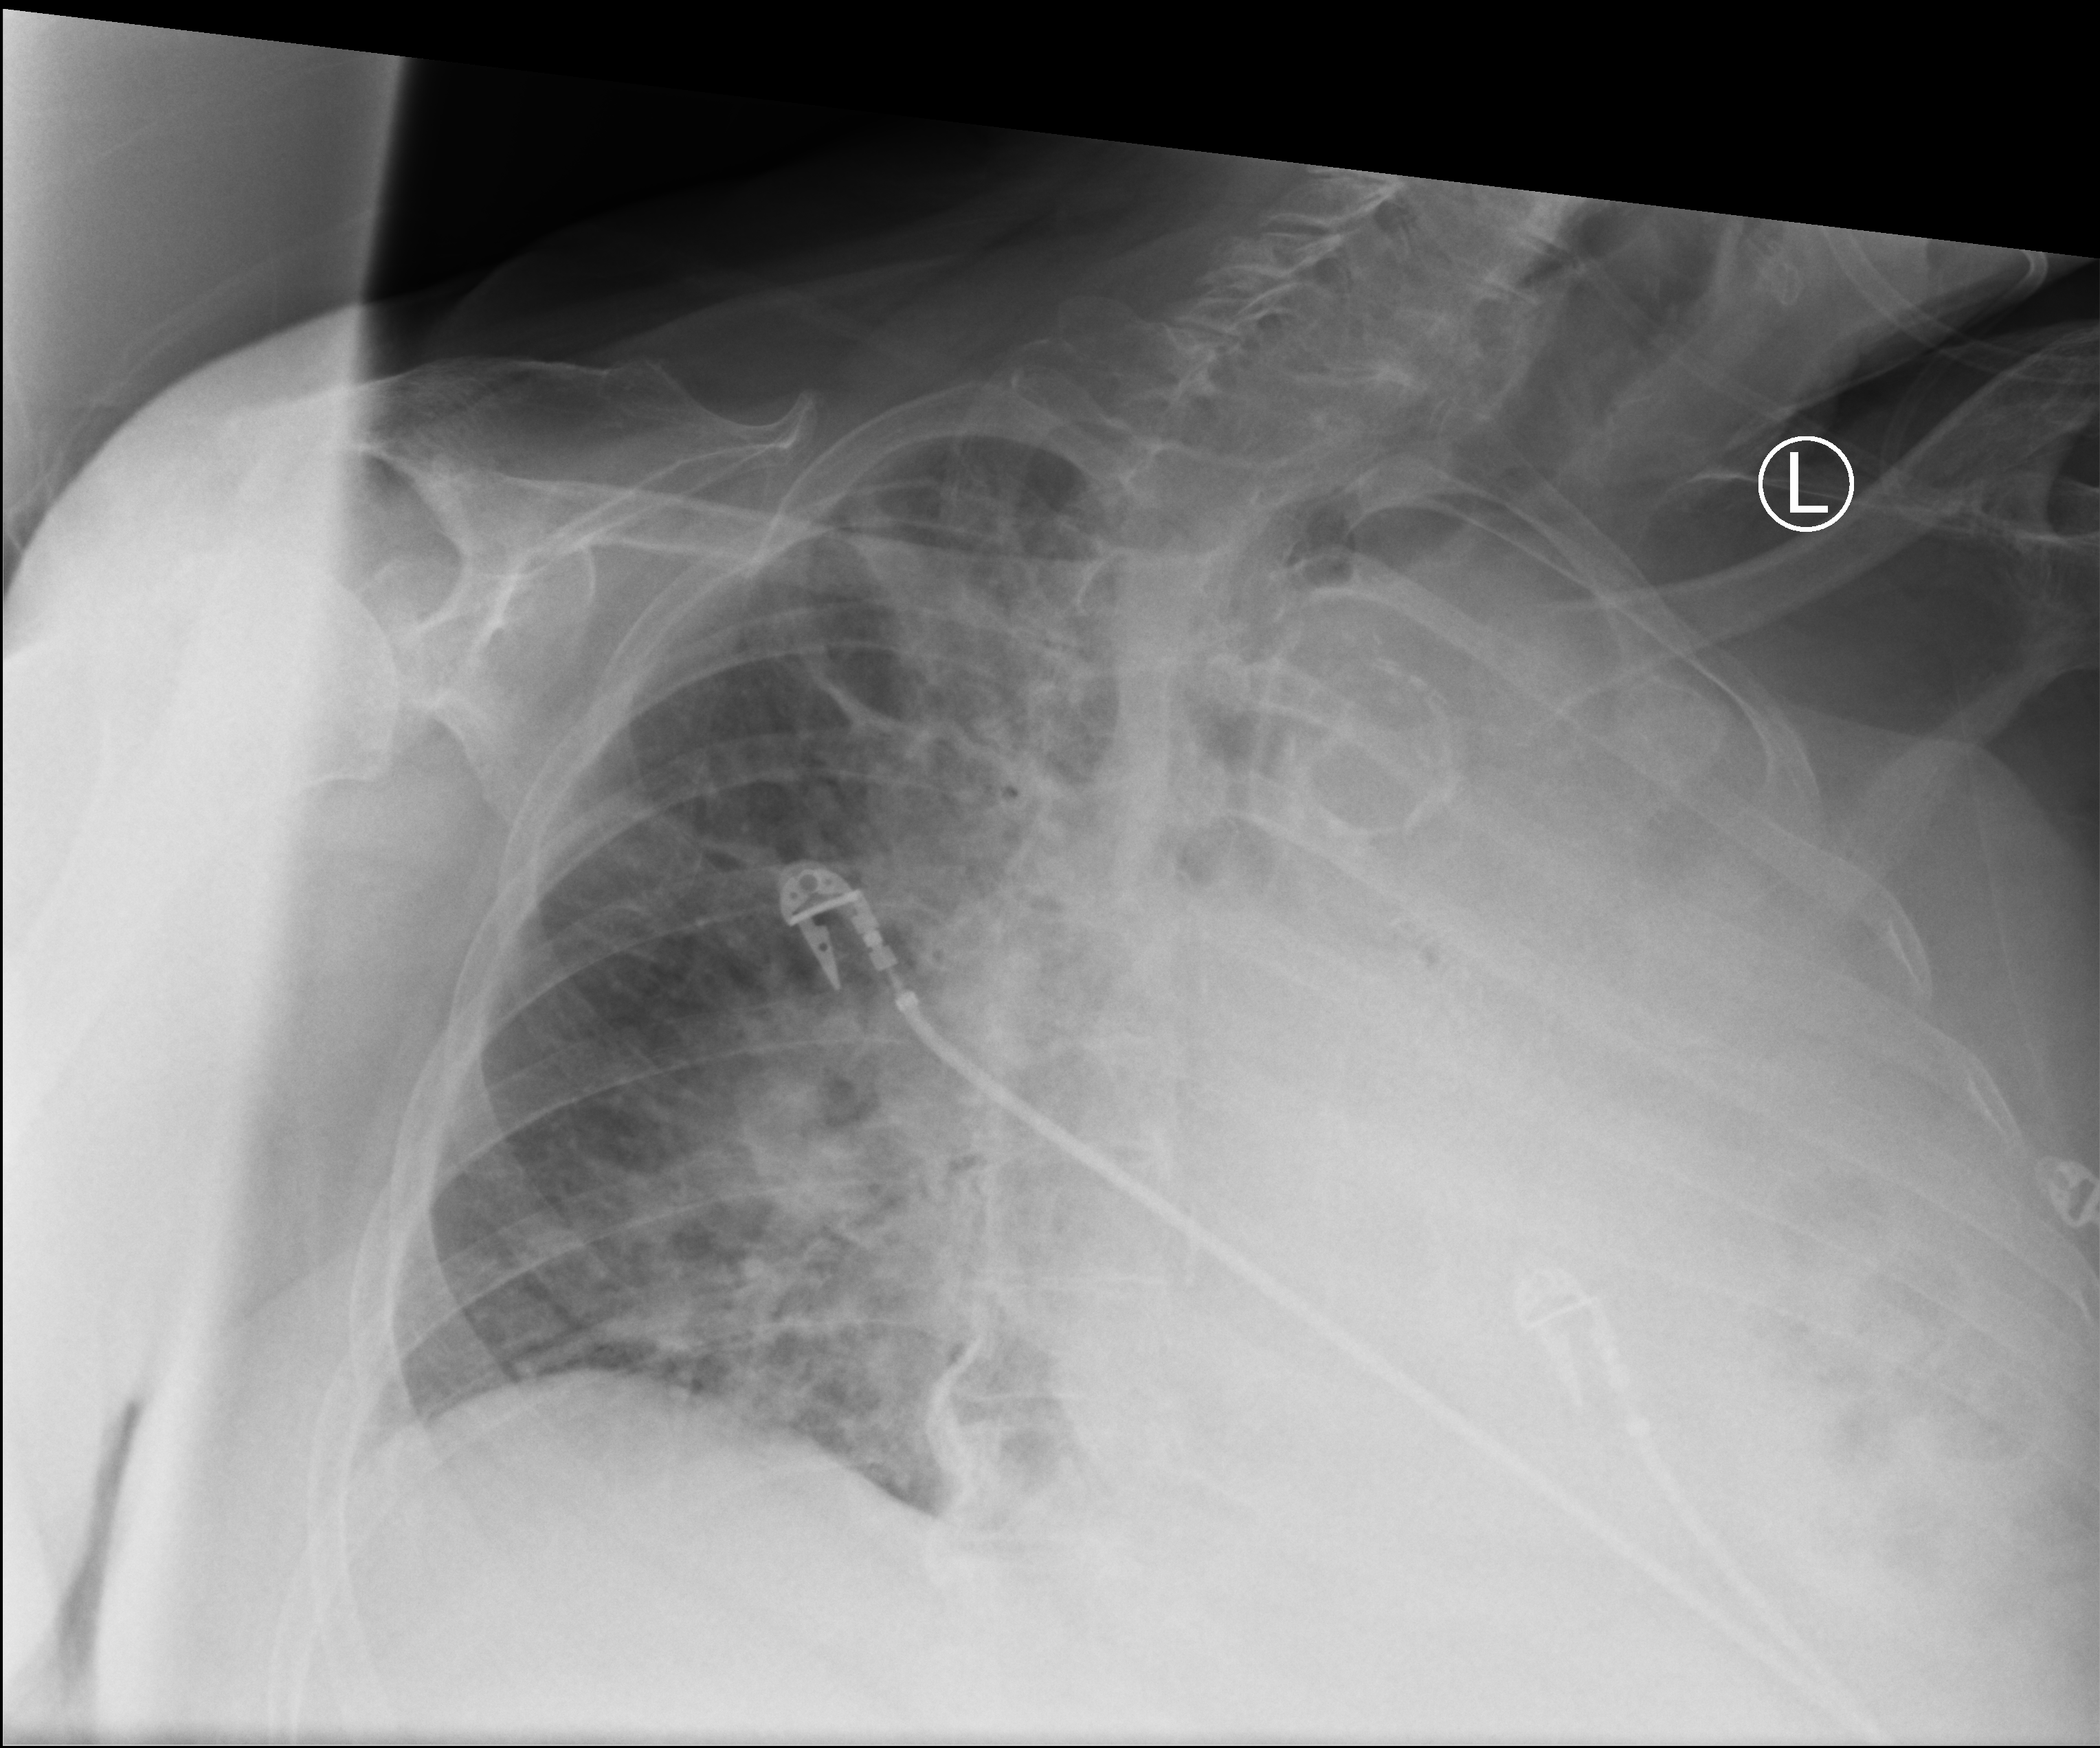
Chest X-ray (portable); anteroposterior (AP) projection. Female patient hospitalised with COVID-19, age 75–90 years.
Admission-level facts for this patient (not findings on this image; timing relative to this image not recorded):
- mechanically ventilated during this hospital stay: no
- length of hospital stay: 5 days
- admitted to intensive care during this hospital stay: yes